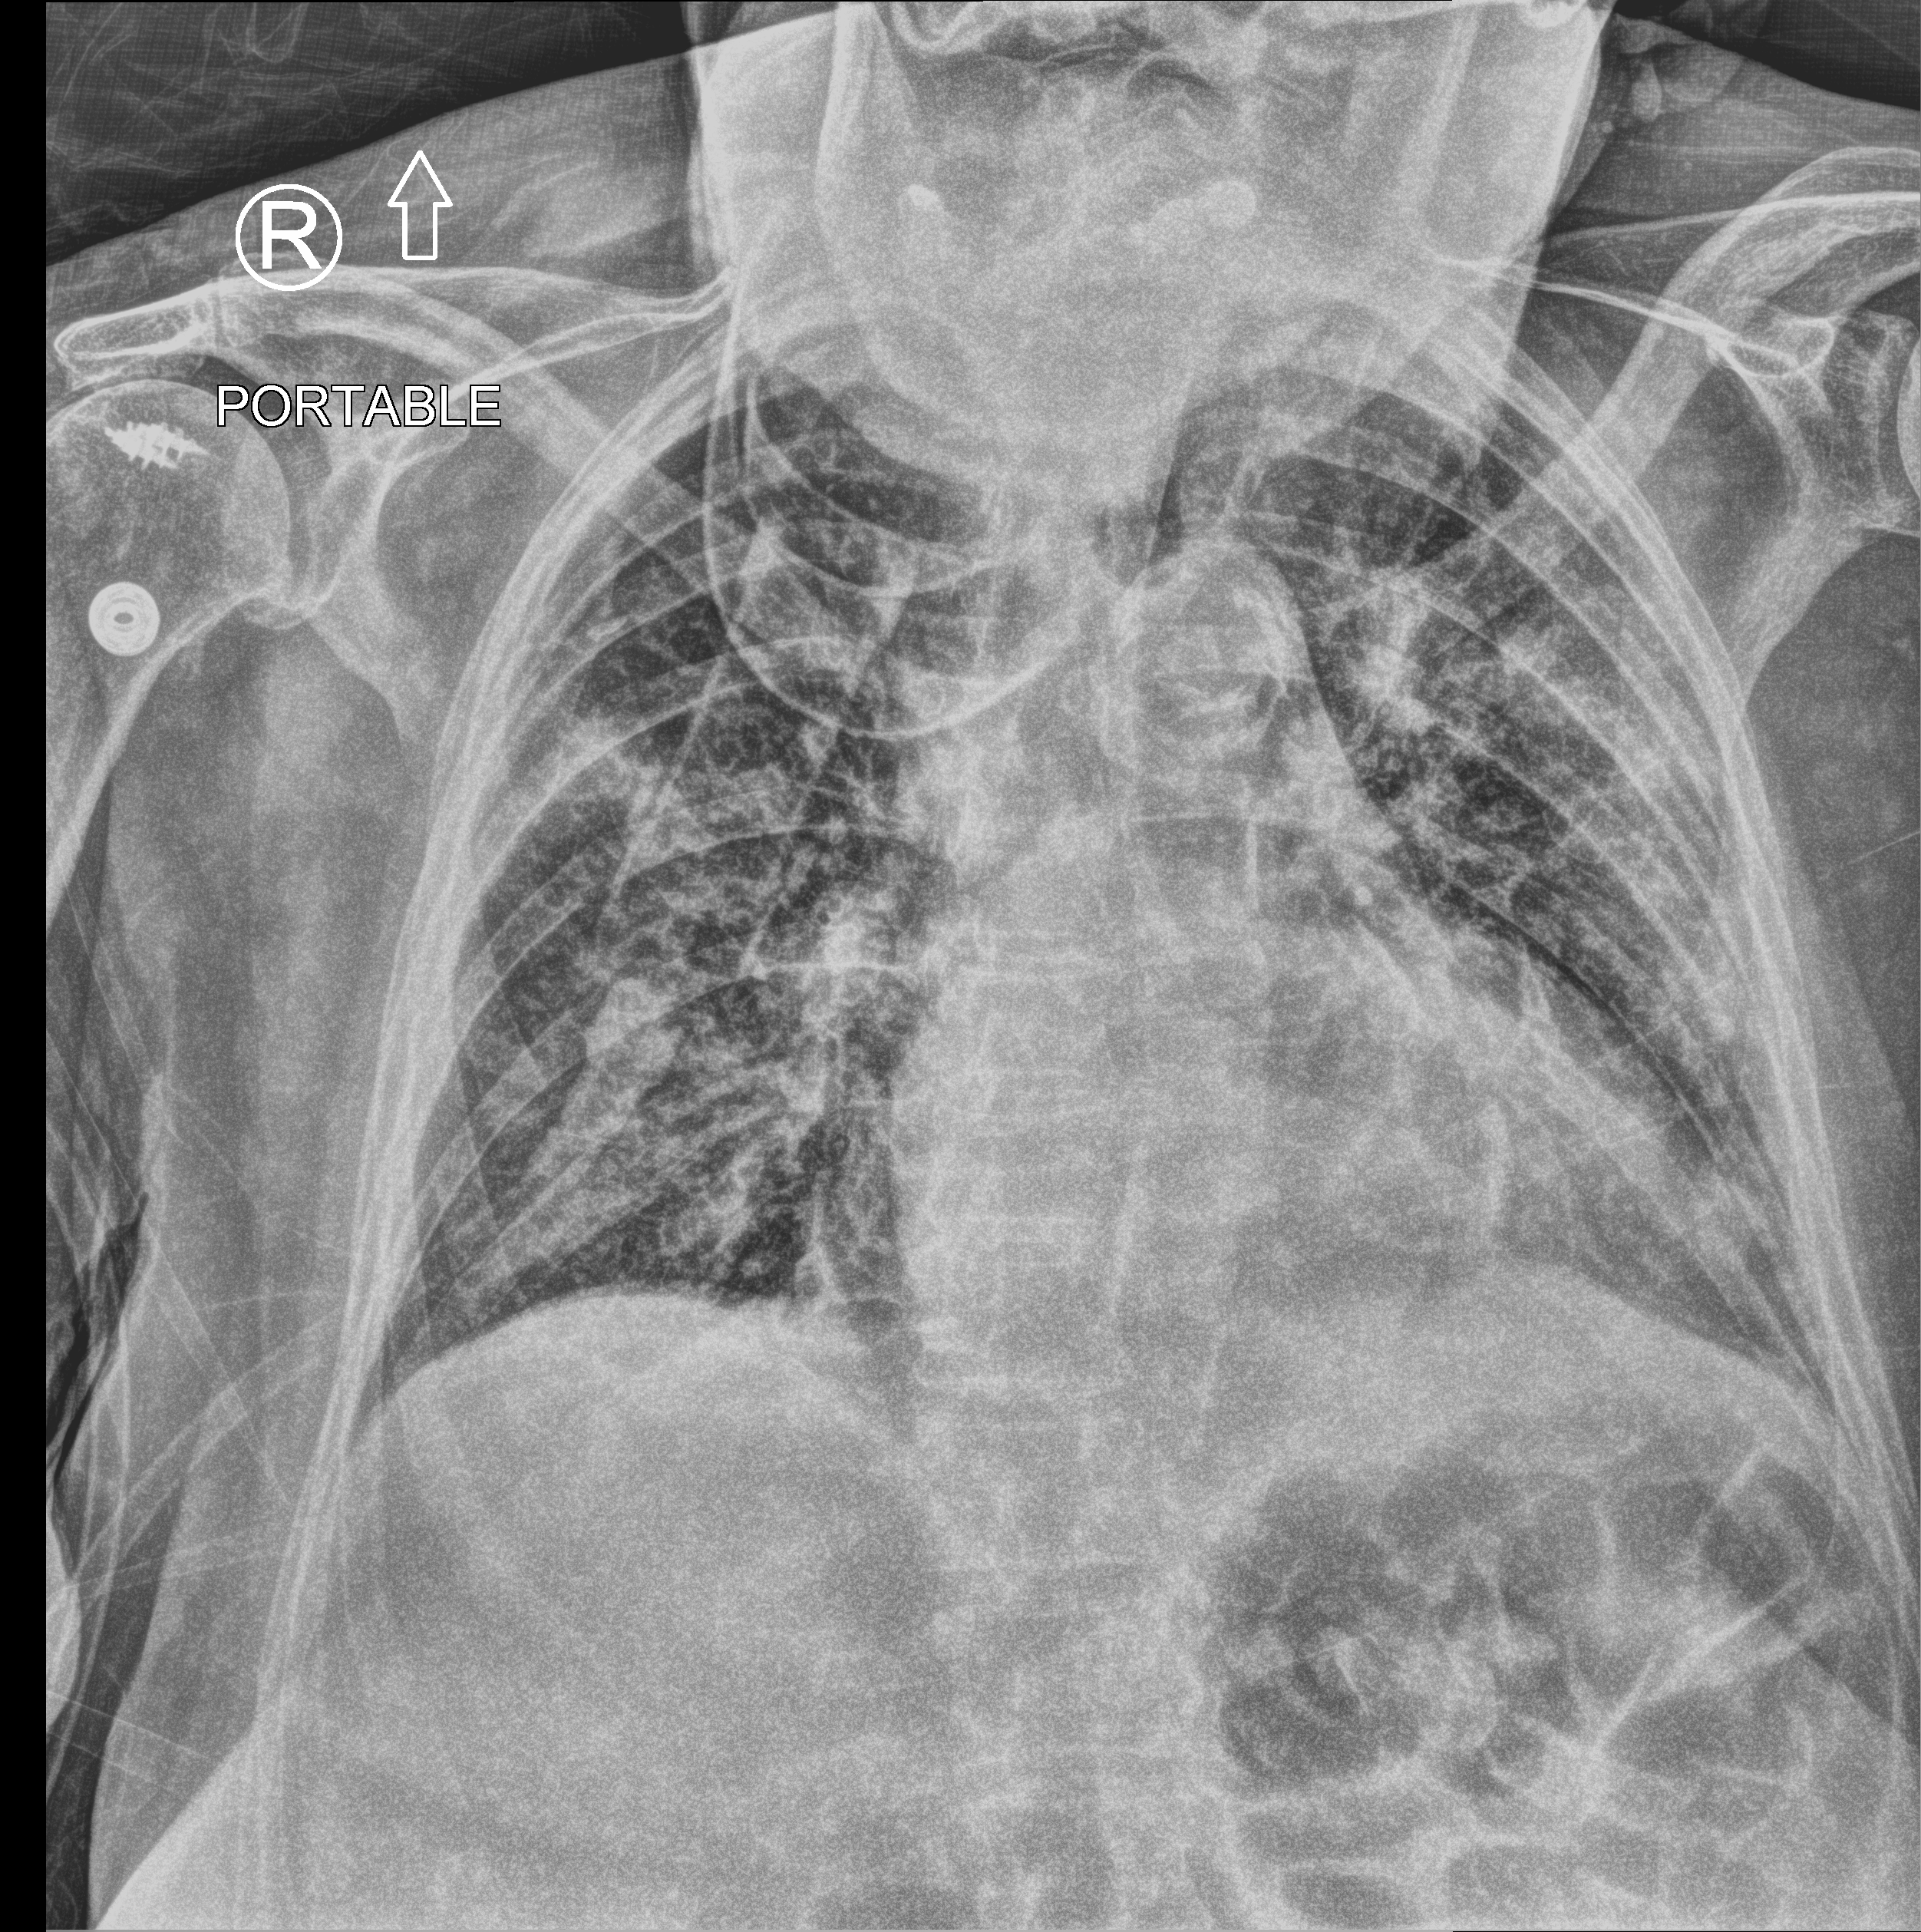
Bedside chest radiograph (computed radiography), anteroposterior (AP) projection. Female patient hospitalised with COVID-19, age 75–90 years.
From the hospital-stay record, not from the radiograph (when in the stay this image was taken is not recorded): COPD (admission record): no; admitted to intensive care during this hospital stay: no; mechanically ventilated during this hospital stay: no.